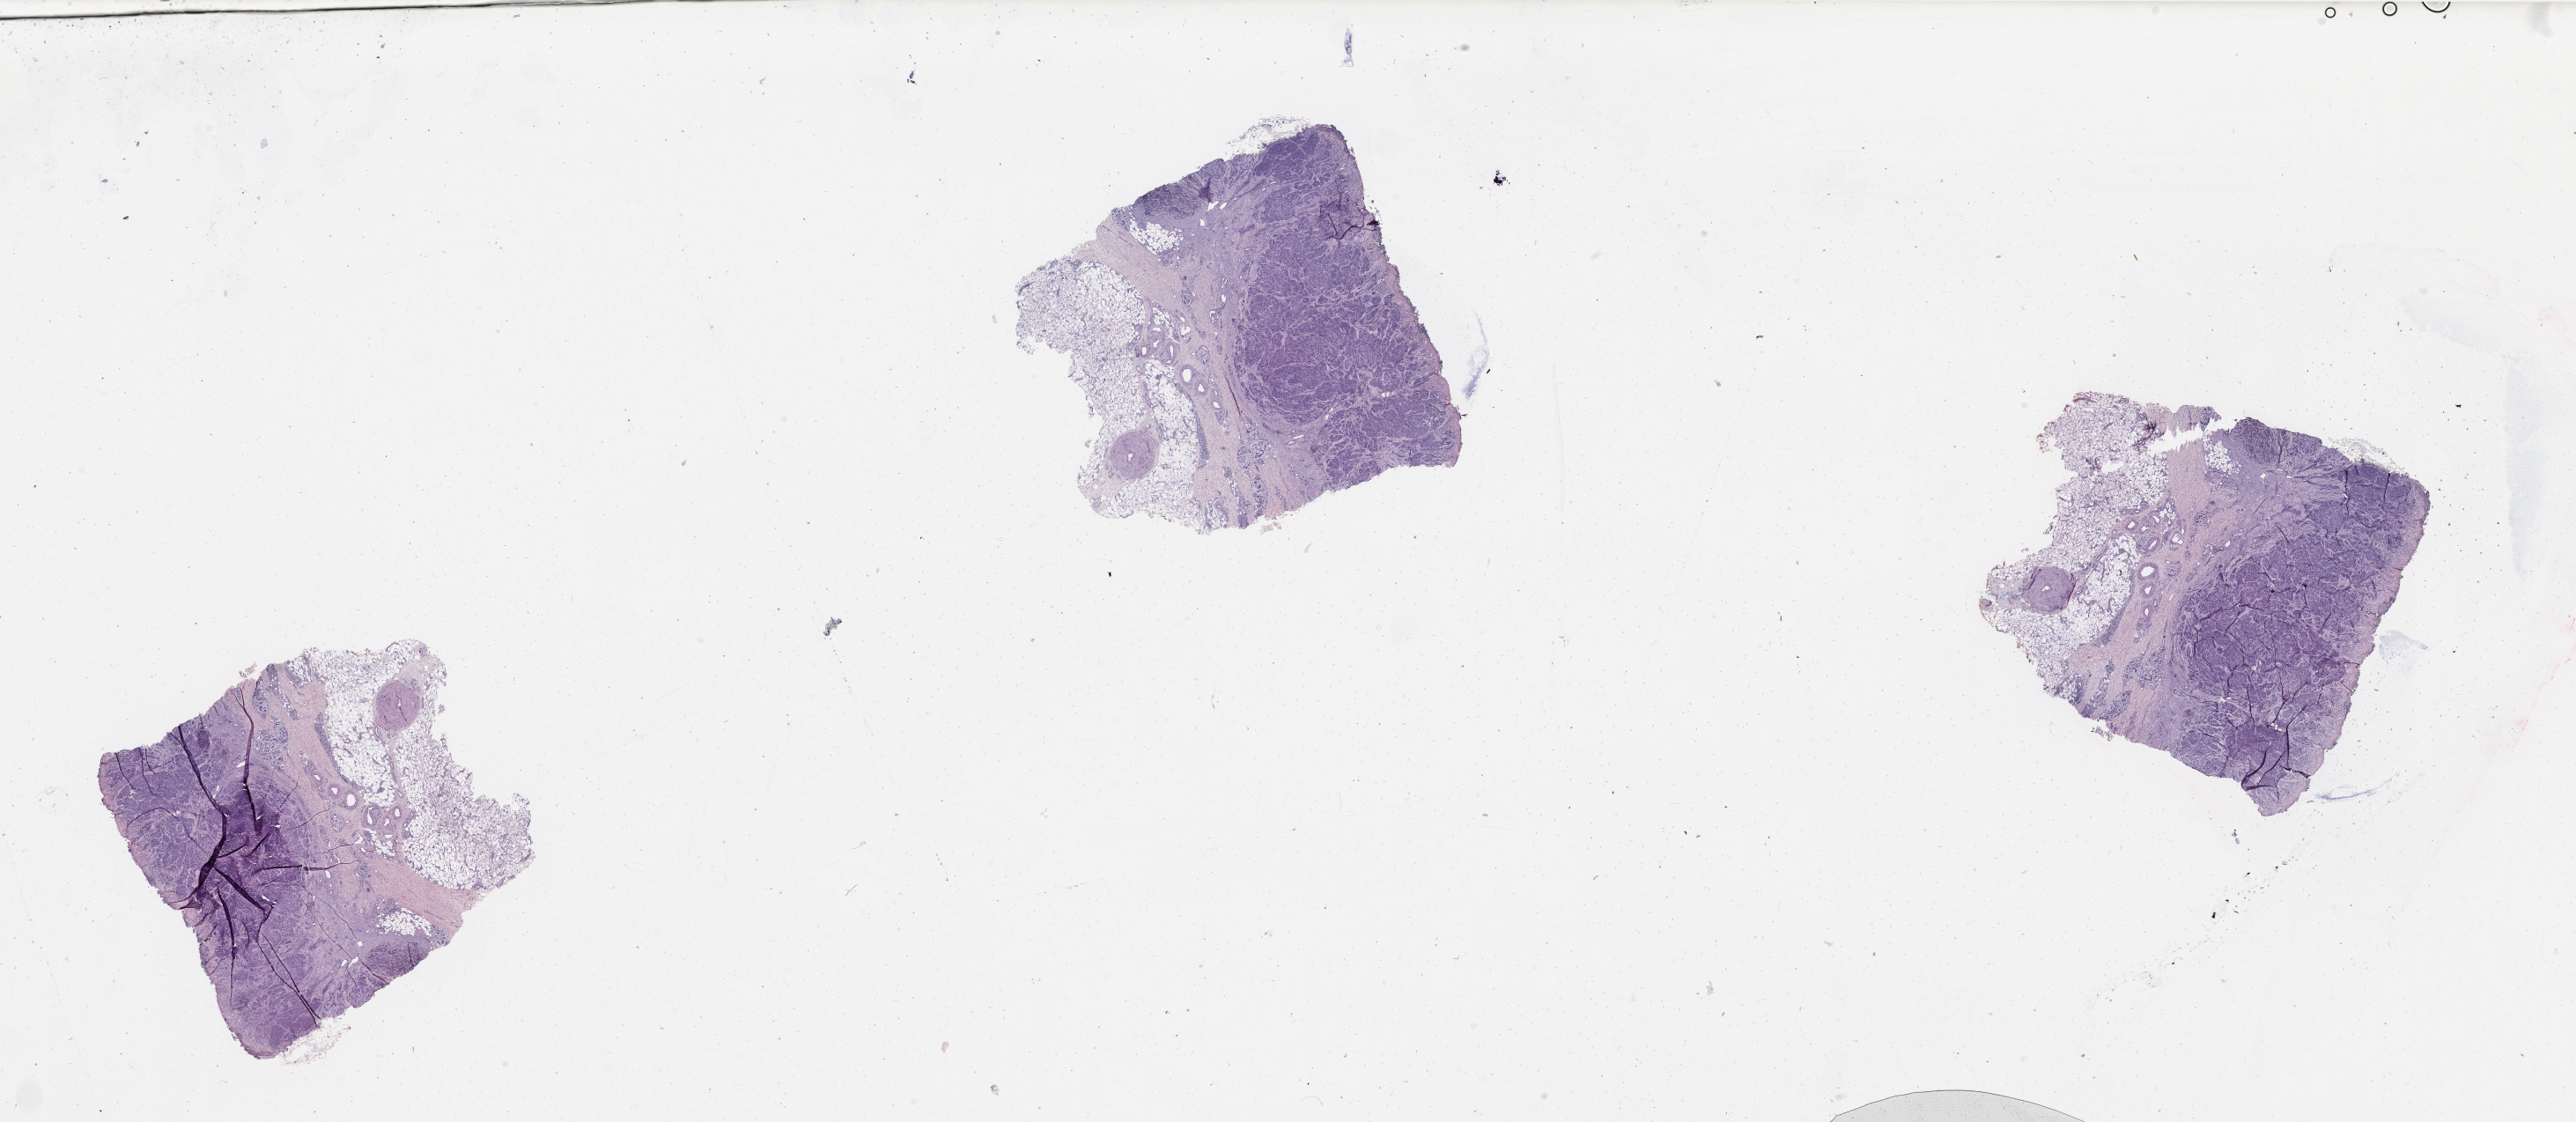
Digitized H&E-stained tissue section (whole slide), whole scanned area (about 46.3 x 20.2 mm) shown as a low-resolution overview; melanoma tumour tissue; sampled site not recorded. Female patient, aged 90 or older.
* AJCC pathologic stage: IIC
* histologic diagnosis: Malignant melanoma, NOS
* primary tumour site (as recorded): extremities